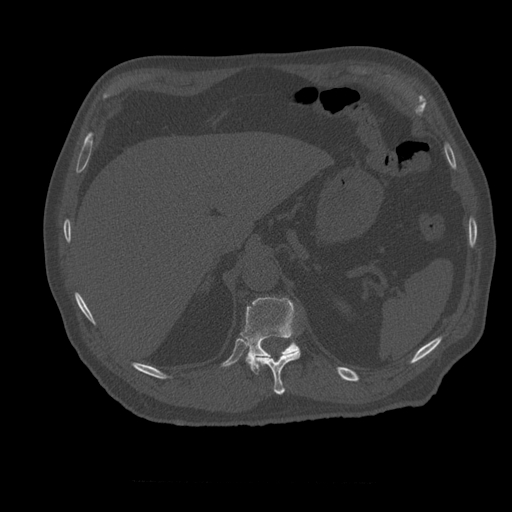
CT including the spine, one axial slice; position 271 of 399 along the scan axis; reconstruction kernel STANDARD; bone window (W 1800 / L 400 HU); 512 × 512 image matrix, field of view 407 × 407 mm. Patient age 73 years. From the clinical record (not read from this slice): primary cancer: prostate.
Annotated regions visible in this slice (semi-automatically segmented with operator editing):
- T11 vertebra: bounding box (x1, y1, x2, y2) in pixels: (255, 351, 301, 395)
- T12 vertebra: (241, 297, 301, 374)